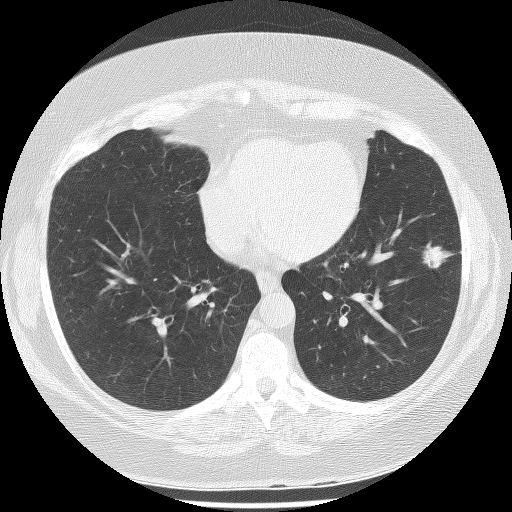
Low-dose screening chest CT, one axial slice. Slice 101 of 233 in the series (ordered by position). 120 kVp. Lung window (W 1500 / L -600 HU). 2.5 mm slice thickness. 512 × 512 image matrix.
Outlined on this slice (expert manual segmentation):
- lesion 1 (tumor, lower lobe of left lung): bounding box [x1, y1, x2, y2] px = [422, 243, 451, 269]